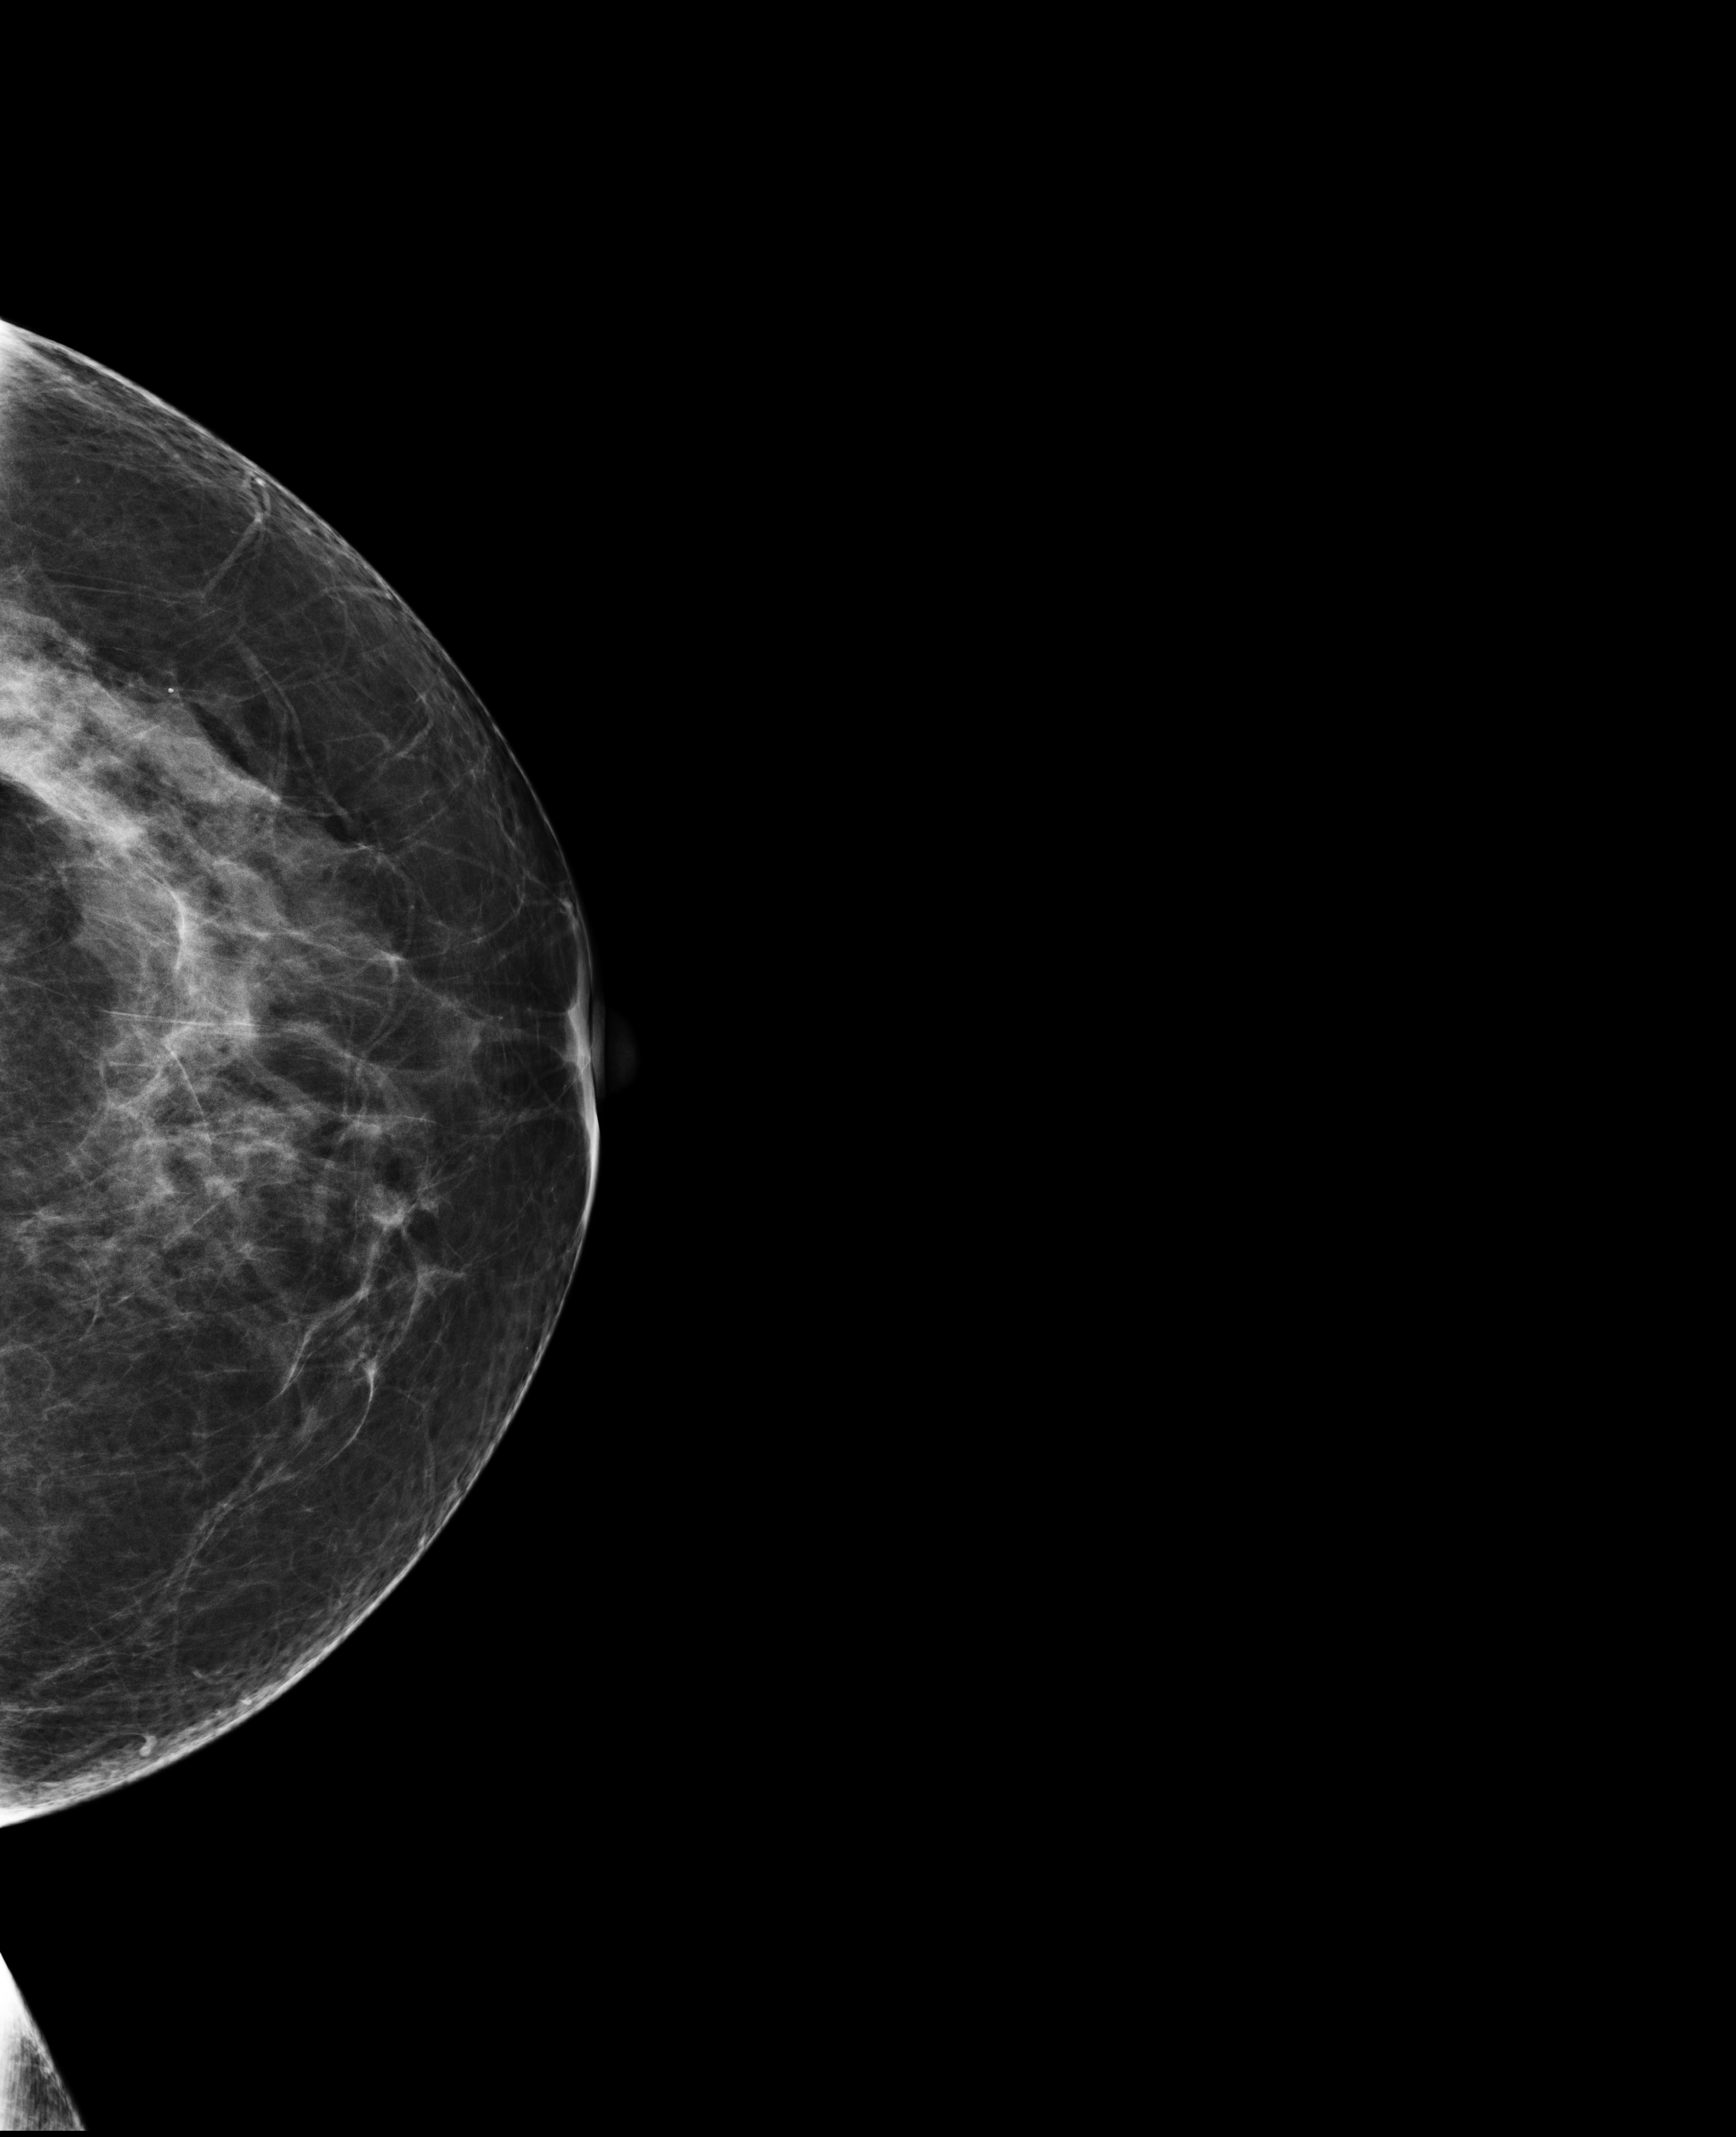
Screening examination; system: Selenia Dimensions. Patient: female, 64 years.
Image type: full-field digital mammogram. Breast: left. Projection: cranio-caudal projection.